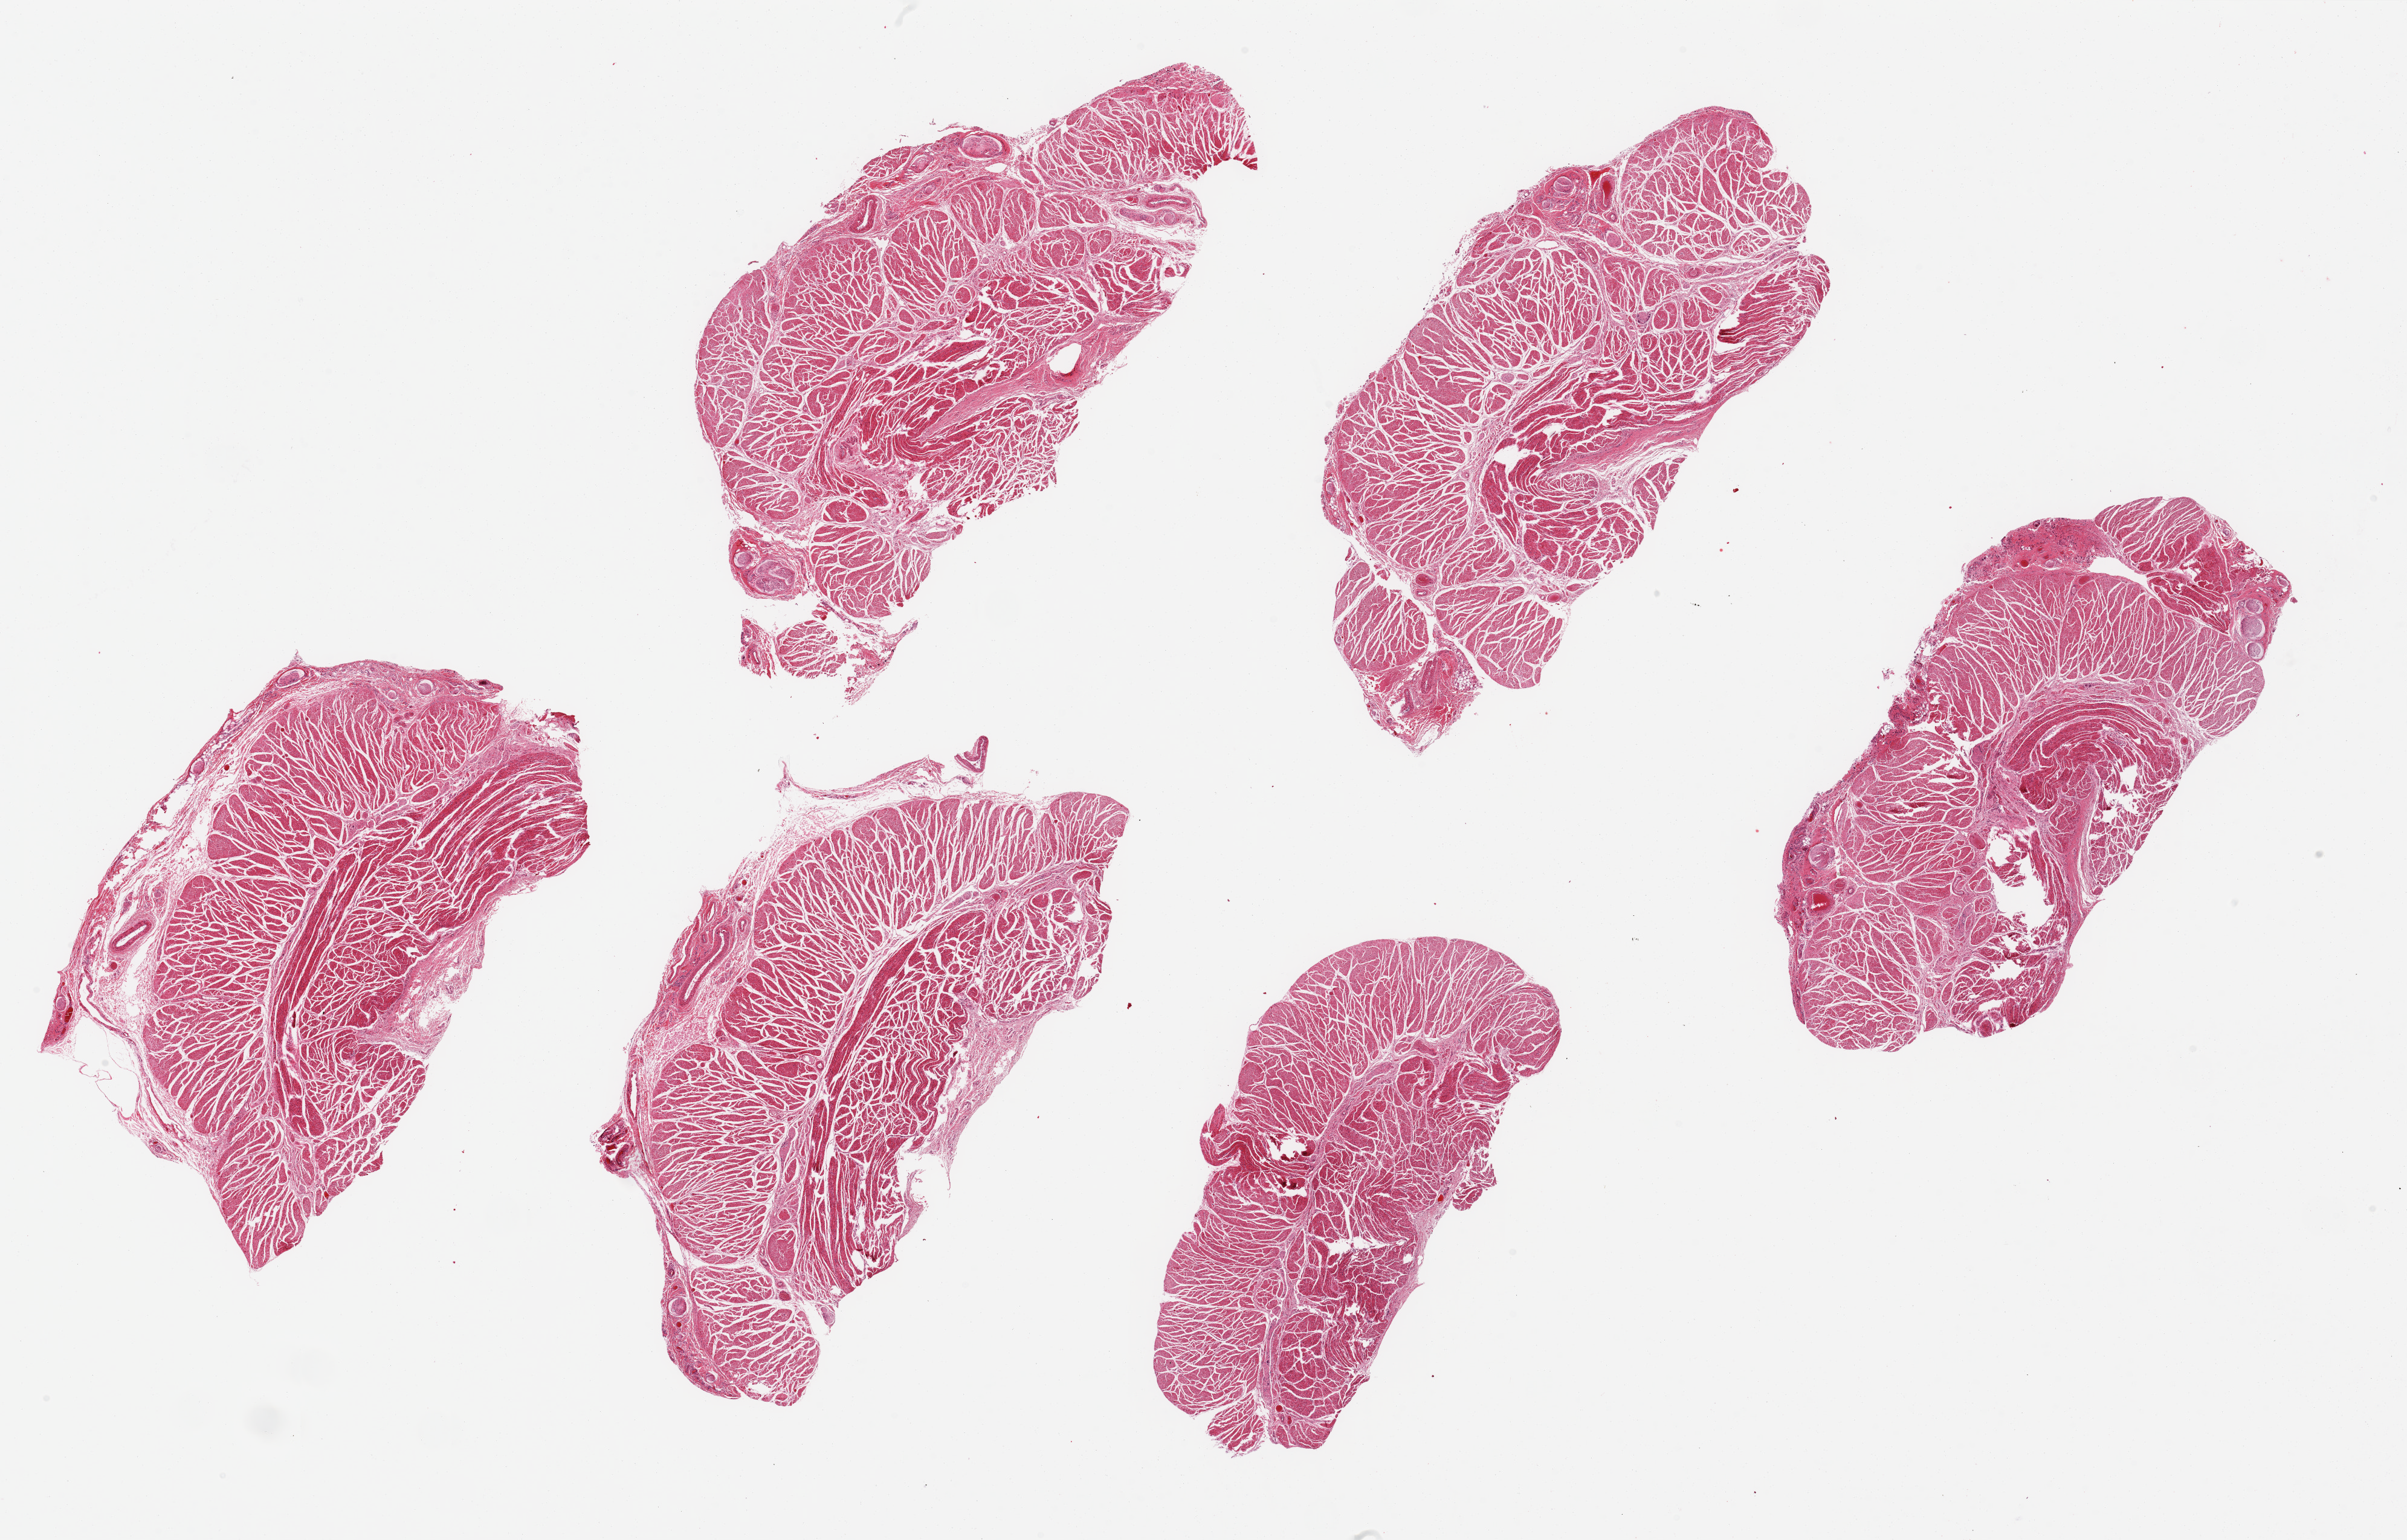
Whole-slide image, haematoxylin and eosin stain, shown as a low-resolution overview of the whole scanned area (about 31.5 x 20.2 mm, slide scanned at 20x); PAXgene-fixed paraffin-embedded (PFPE) section; target tissue: esophageal muscle; donor tissue sample. Donor: female.
Review note (as recorded): 6 pieces up to 9x4 mm.